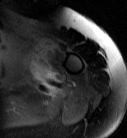
MRI of an extremity soft-tissue mass, one axial slice; T2-weighted fat-saturated; MR volume resampled by the dataset authors to the PET/CT grid (not the native acquisition matrix); 3.27 mm slice thickness; 127 × 138 image matrix, field of view 124 × 135 mm. Female patient. From the clinical record (not read from this slice): histological type: pleiomorphic leiomyosarcoma; grade: high; site of the primary tumour: left biceps.
Annotated regions visible in this slice (expert contour drawn on MRI and transferred to this co-registered scan by the dataset authors):
- gross tumour volume including surrounding oedema: bounding box (x1, y1, x2, y2) in pixels: (31, 41, 55, 83)